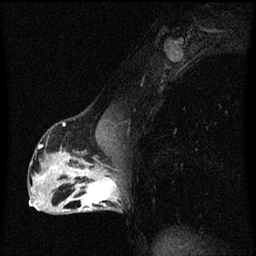
Breast MRI (dynamic contrast-enhanced), one sagittal slice; slice 33 of 60 in the series (ordered by position); dynamic contrast-enhanced series, image 2 of 3 at this slice position (ordered by acquisition); 1.5 T; TE 4.2 ms, TR 8.4 ms; 256 × 256 image matrix, field of view 200 × 200 mm. Female patient, age 40 years.
Outlined on this slice (semi-automatically segmented with operator editing):
- analysis volume of interest (the breast-tissue region the enhancement analysis was run in; not a lesion): box from (x=76, y=172) to (x=120, y=213) px
- tumour enhancement mask (voxels above the 70 % enhancement threshold inside the analysis volume of interest): (x=76, y=172)–(x=118, y=211)